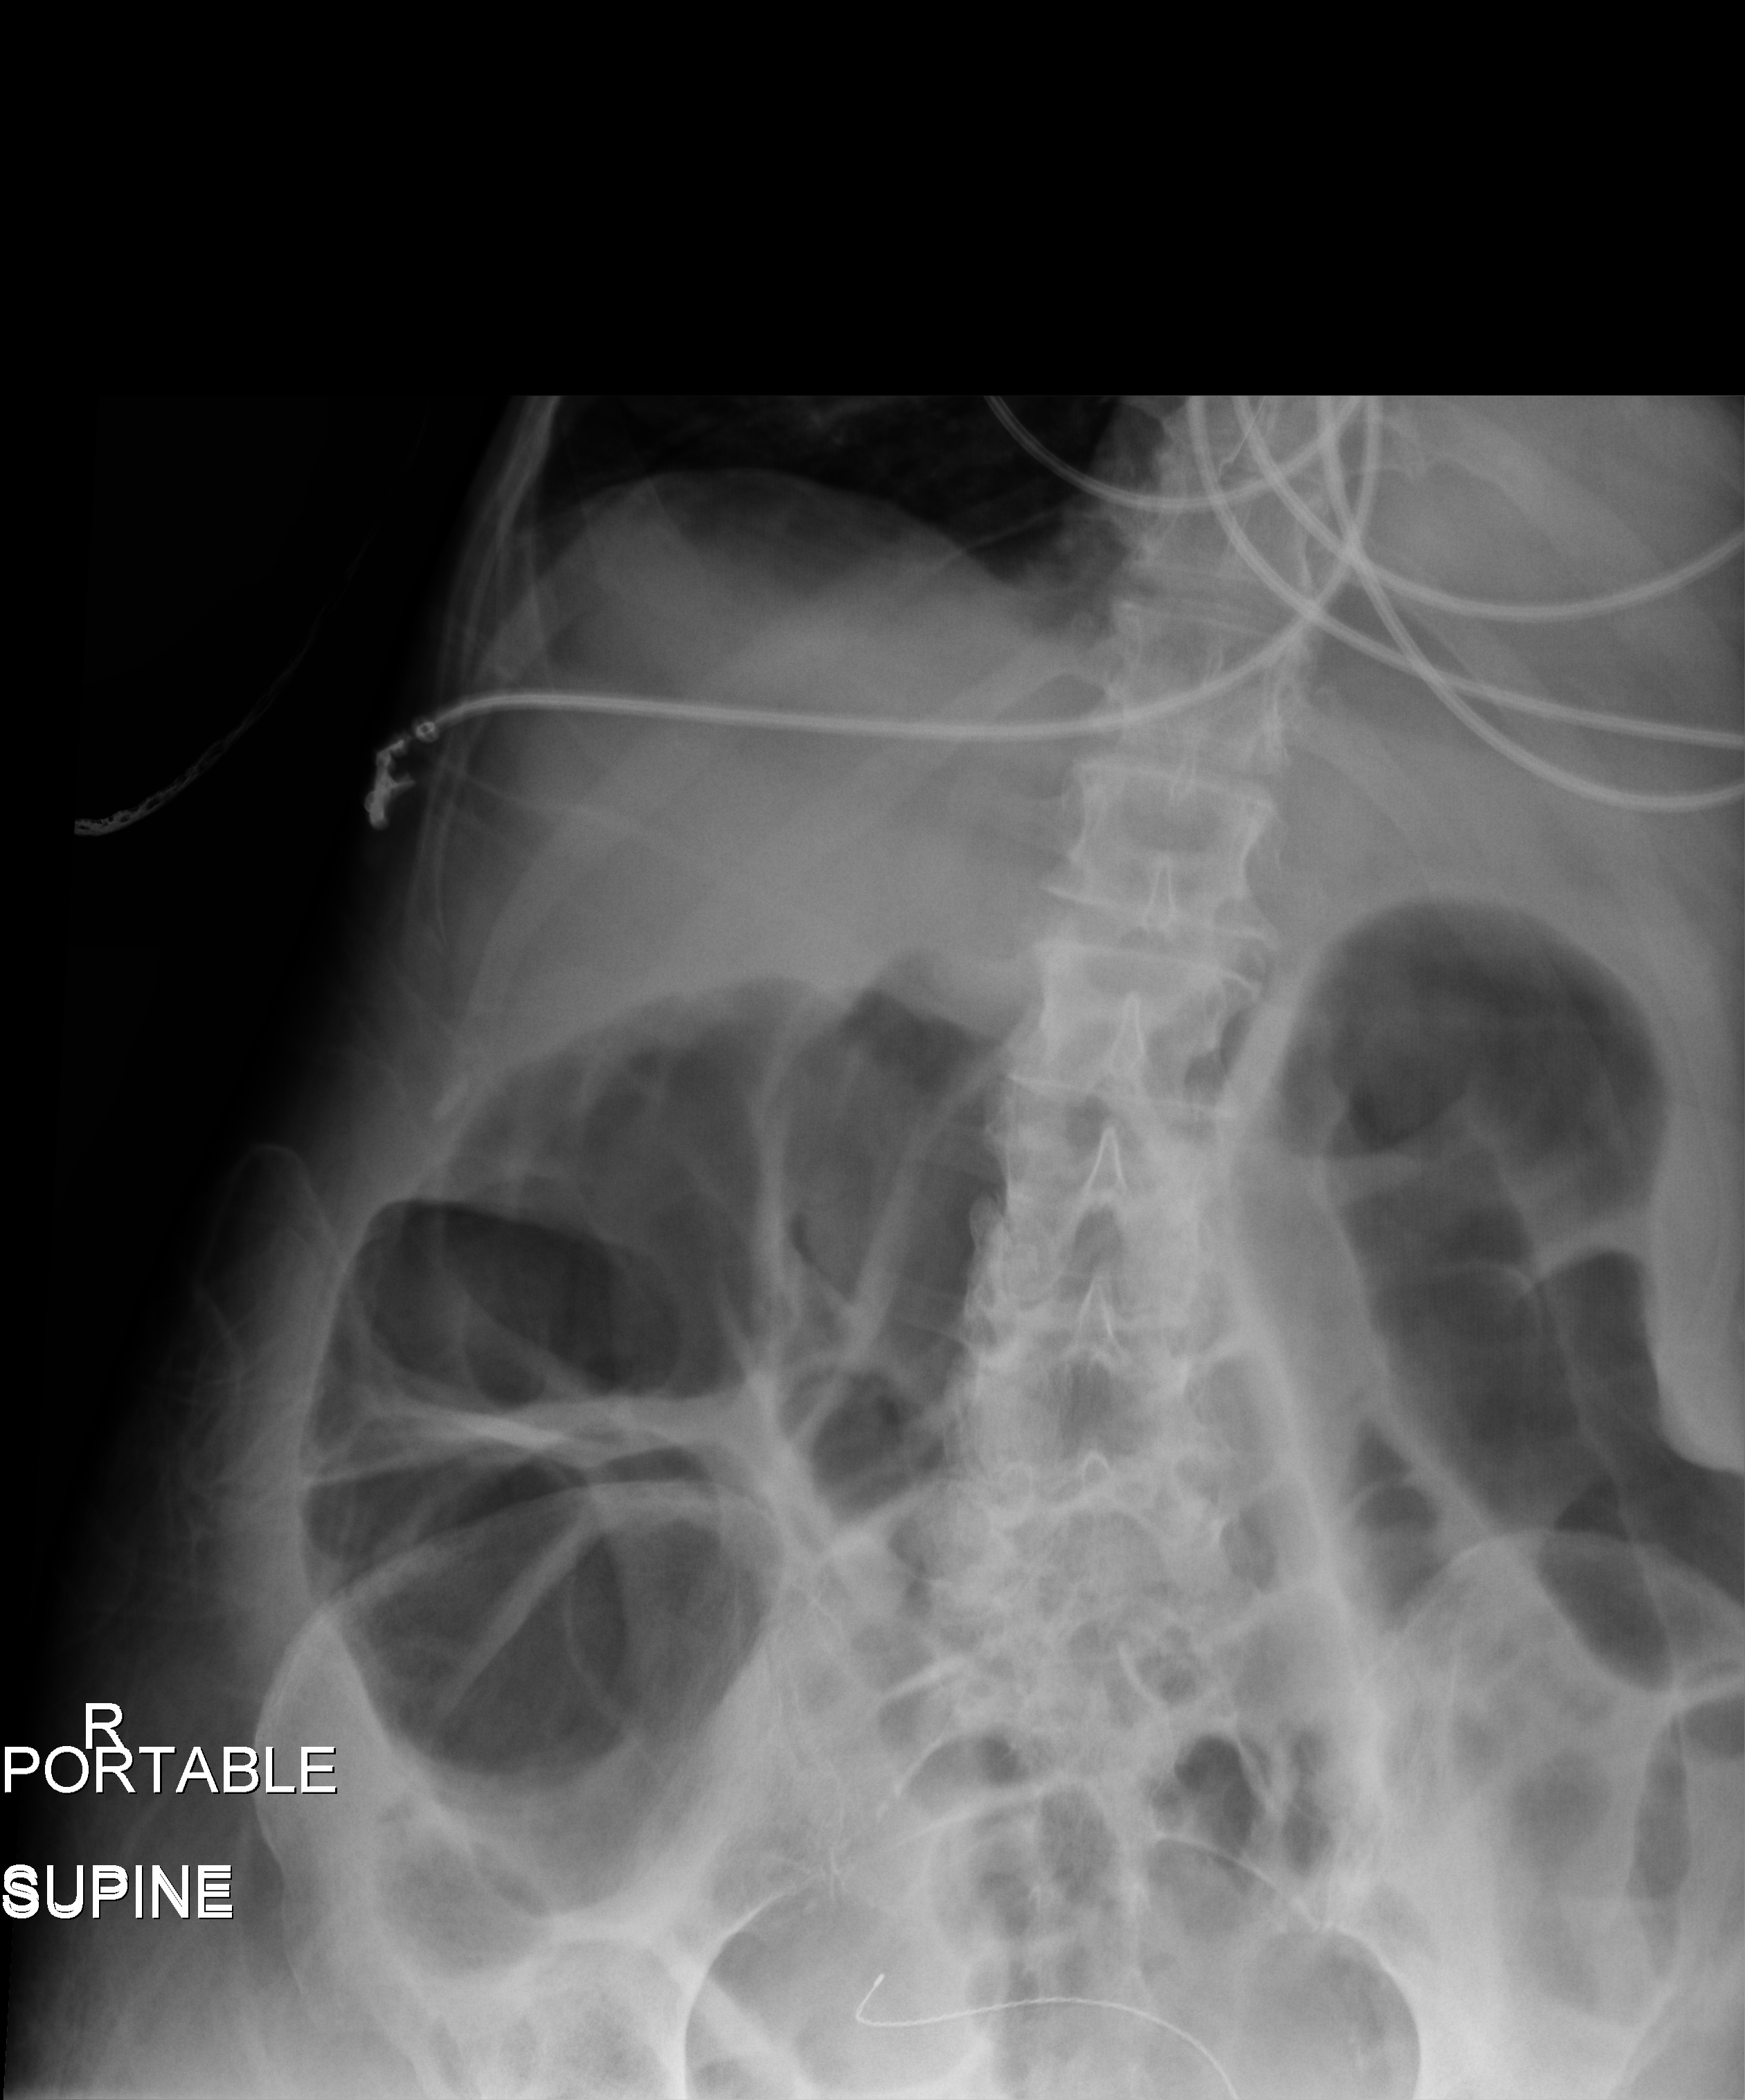
Abdomen X-ray (portable); anteroposterior (AP) projection. Patient hospitalised with COVID-19; female, aged 60–74 years.
Hospital-stay facts (about this admission, not read from this image; timing relative to this image not recorded): mechanically ventilated during this hospital stay: yes.